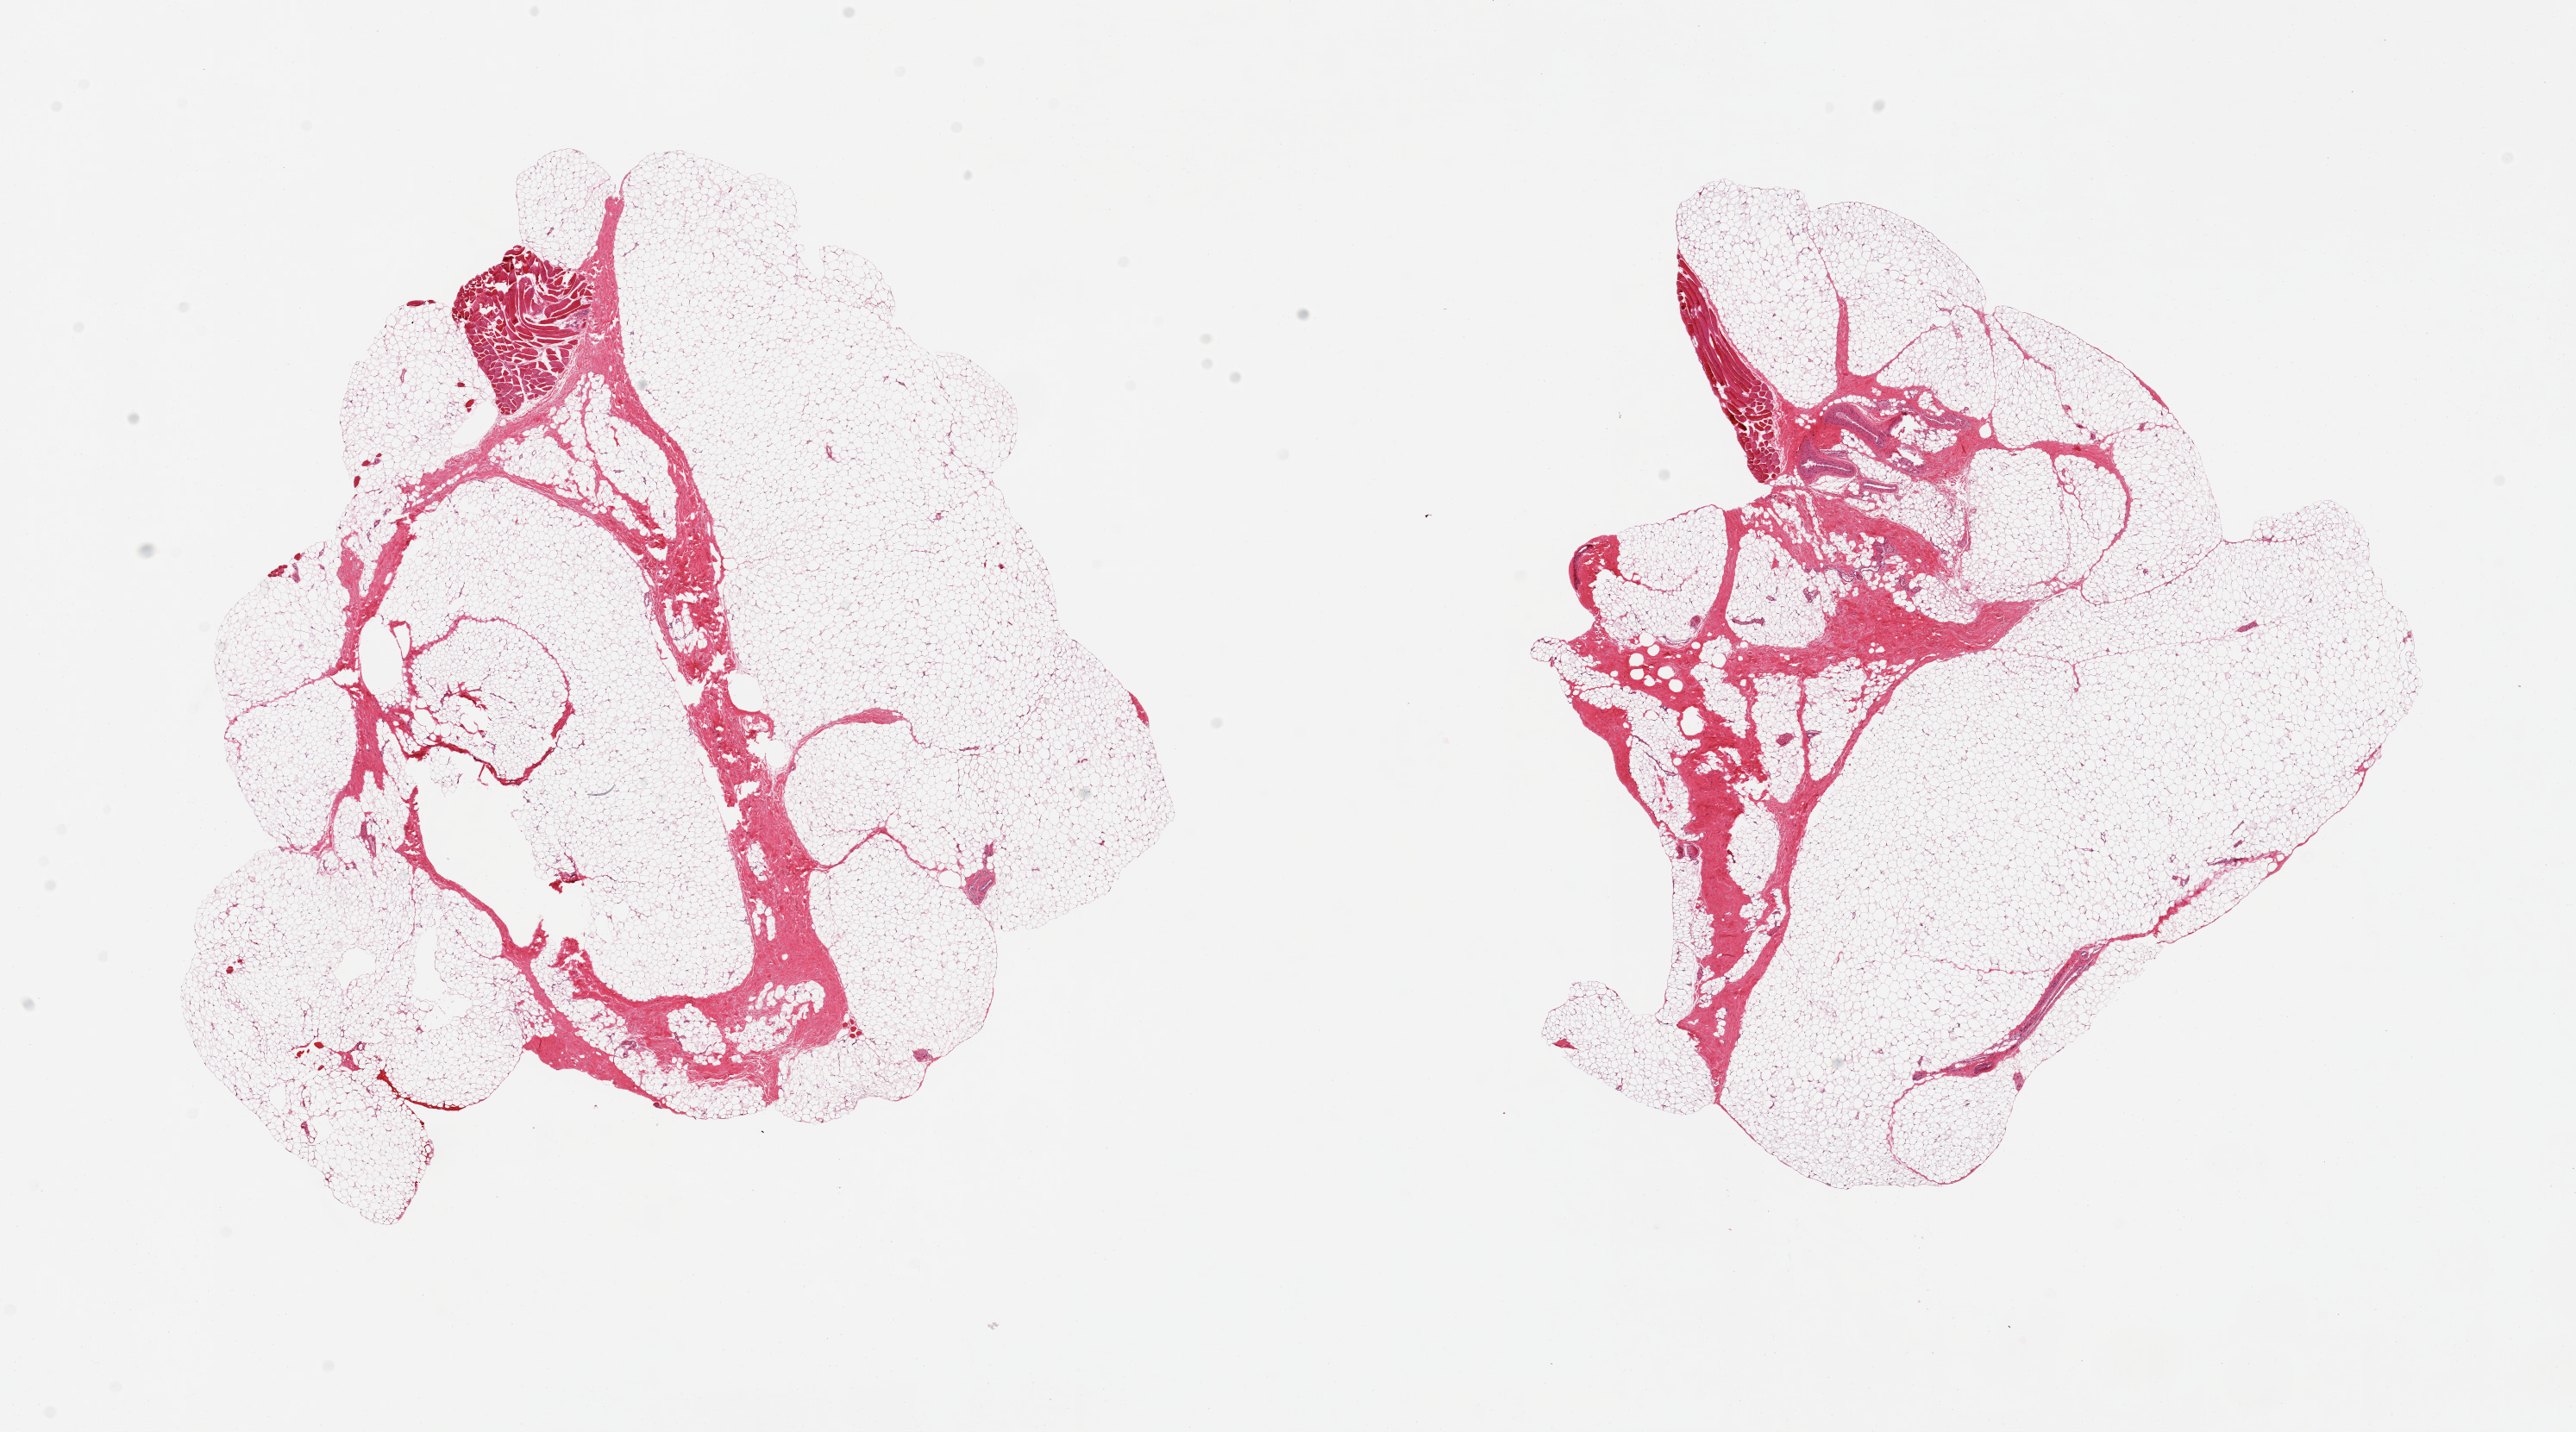
Digitized H&E-stained section, brightfield — whole scanned area (about 23.6 x 13.1 mm) shown as a low-resolution overview, PAXgene-fixed, paraffin-embedded tissue, sampled site (target tissue): breast, donor tissue sample. Donor sex: male.
* review note (as recorded): 2 pieces, 10x9 & 8x8mm; focal skeletal muscle in both aliquots up to ~2x1mm